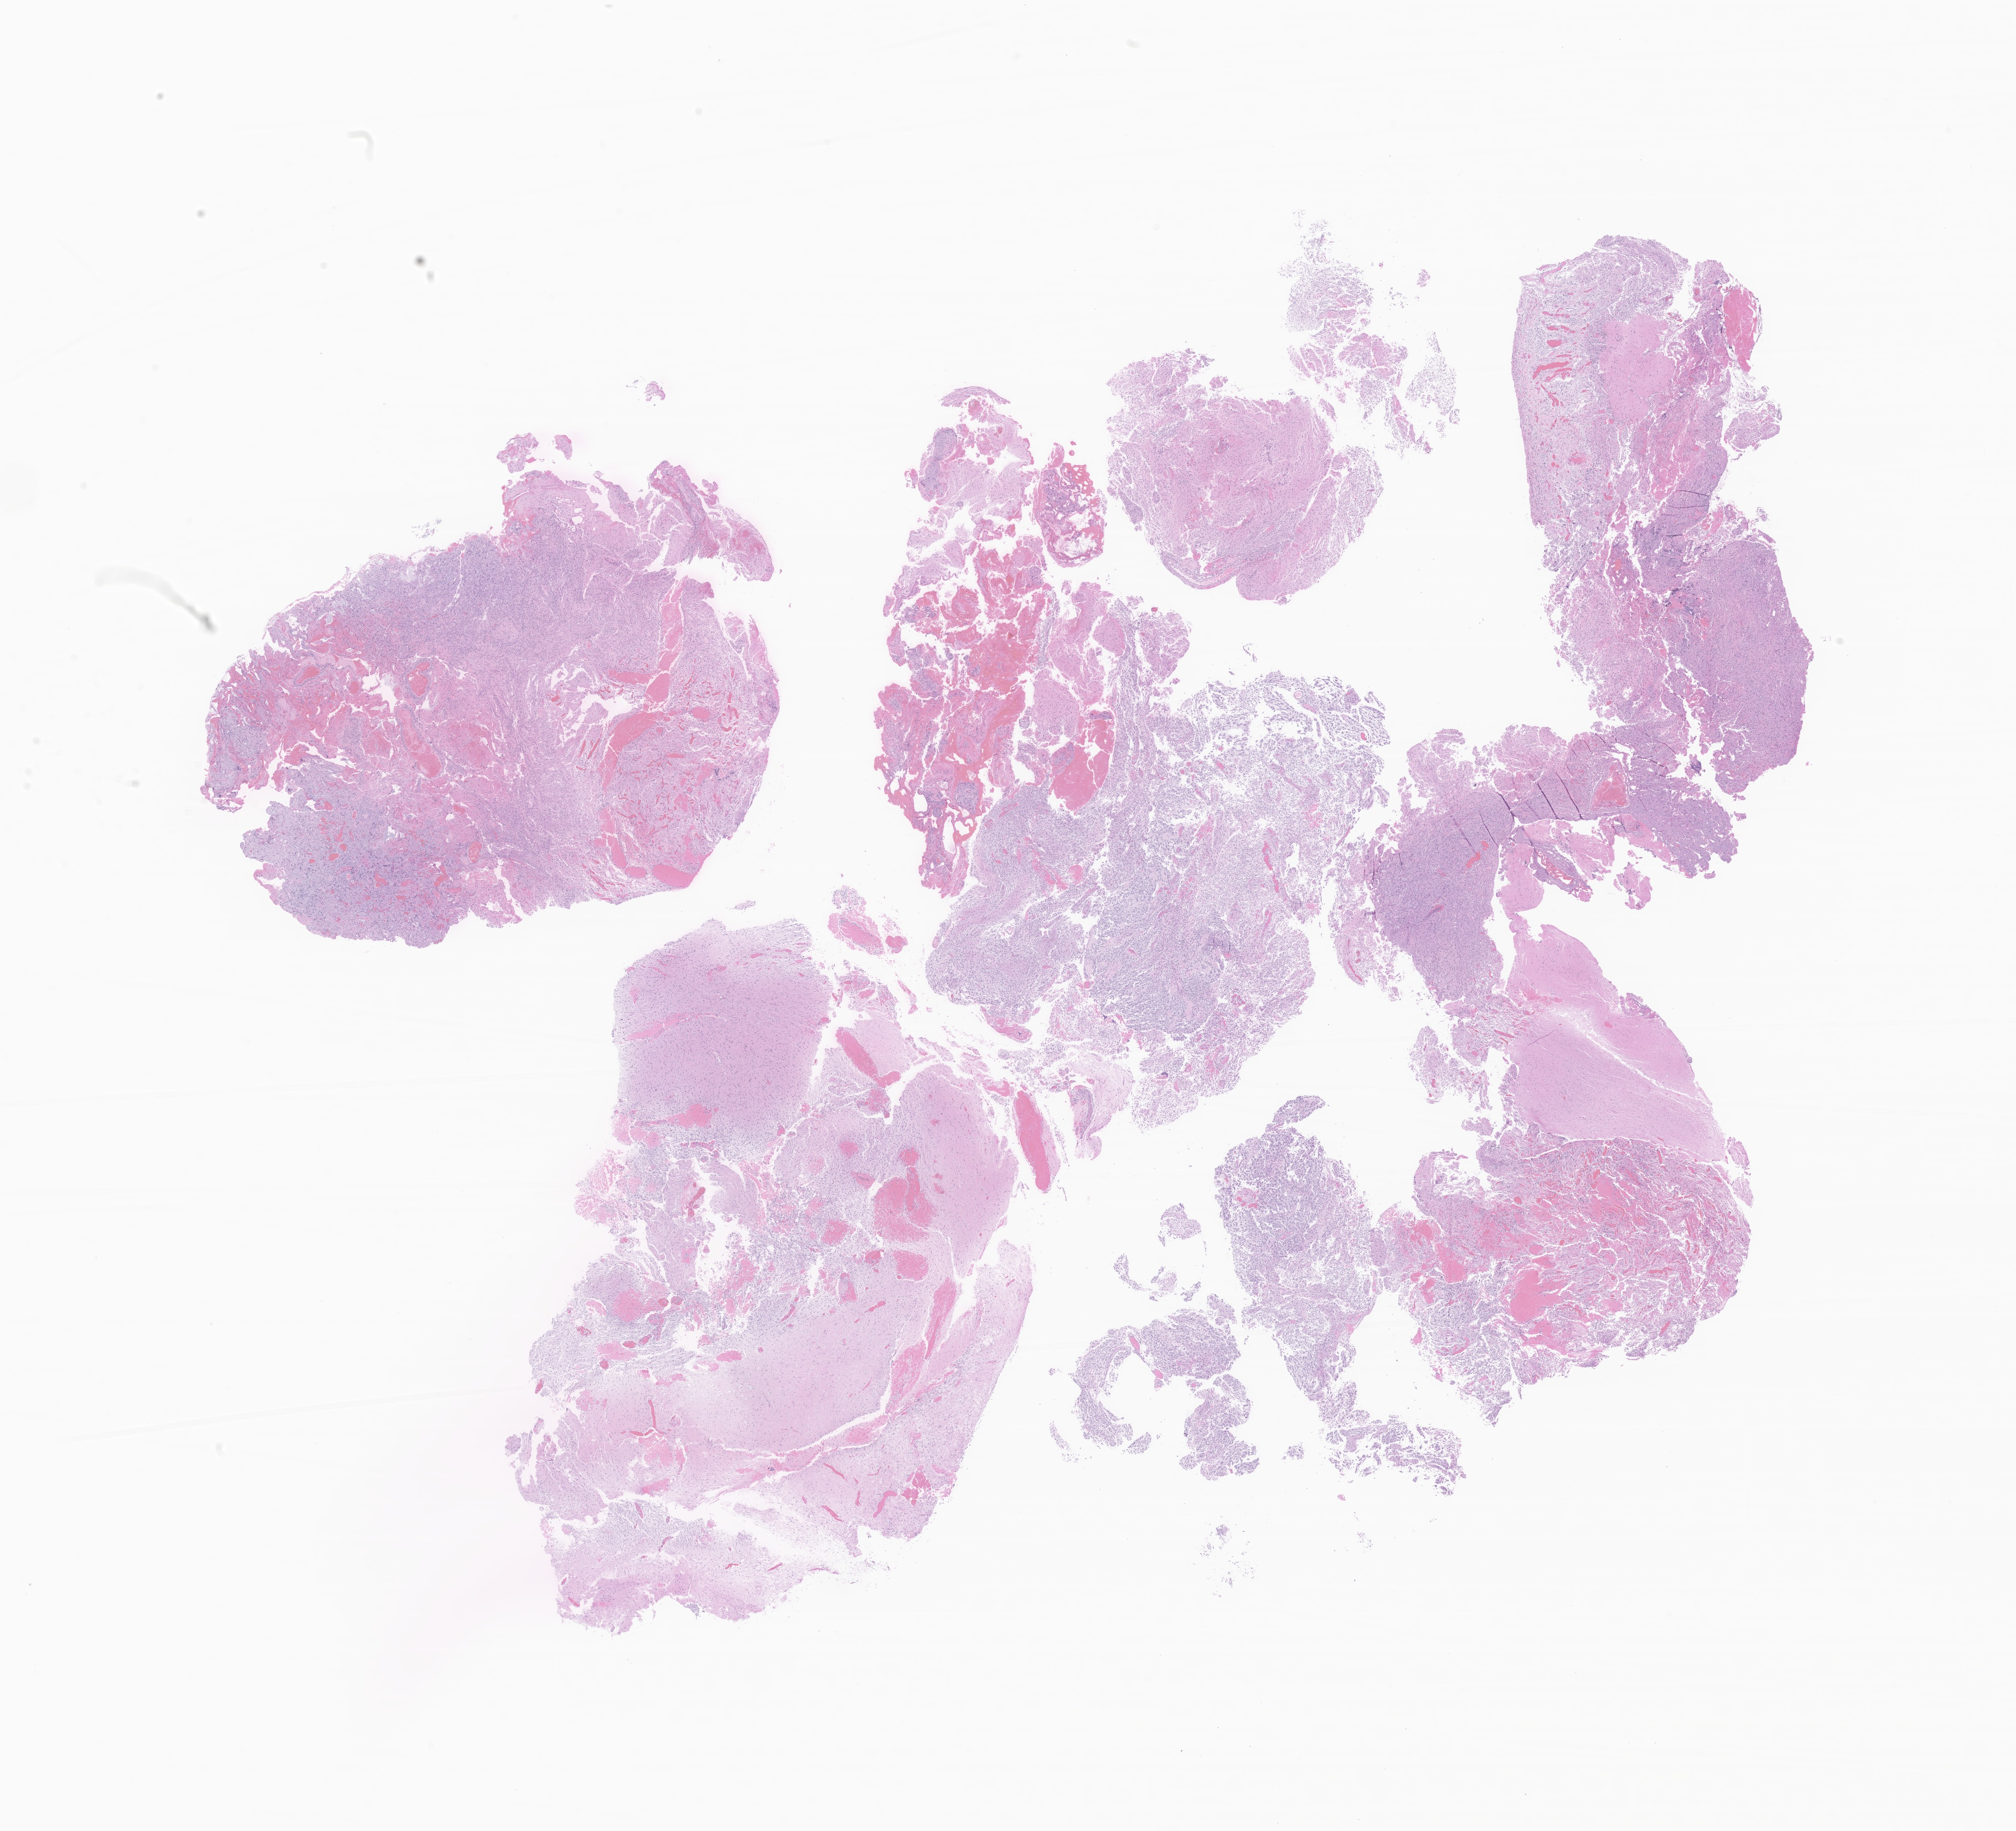
Digitized hematoxylin and eosin (H&E)-stained section of tumor tissue from the brain — whole scanned area (about 19.3 x 17.5 mm) shown as a low-resolution overview, FFPE section. Female patient, age 33 months (2 years 9 months).
* diagnosis (ICD-O-3 morphology term): Pilocytic astrocytoma